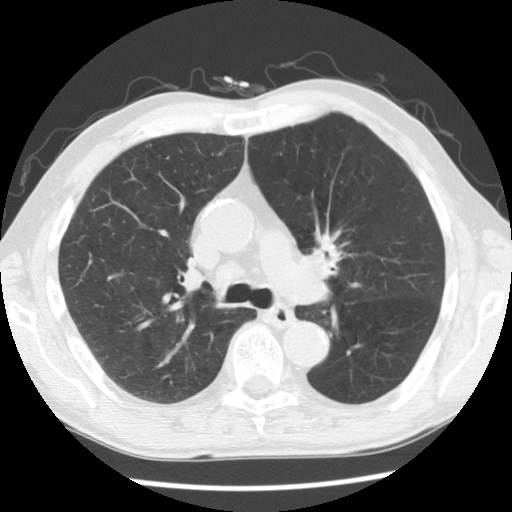
Low-dose screening chest CT, axial slice; first (baseline) screen; lung window (W 1500 / L -600 HU); 2.5 mm slice thickness; standard (soft-tissue) reconstruction kernel (STANDARD); slice 81 of 132 in the series; 512 × 512 image matrix, field of view 330 × 330 mm. Male, age 68 years at enrolment. Current smoker at enrolment.
Expert-annotated lung lesion, bounding box <298,224,355,279> (left, top, right, bottom; pixels). No non-calcified nodule or mass ≥4 mm was recorded by the screening reader at this exam. Official screen result: negative screen, minor abnormalities not suspicious for lung cancer. Participant outcome: lung cancer diagnosed 215 days after this screen — squamous cell carcinoma, NOS, left hilum, stage IIB (AJCC 6th edition), 32 mm at pathology.